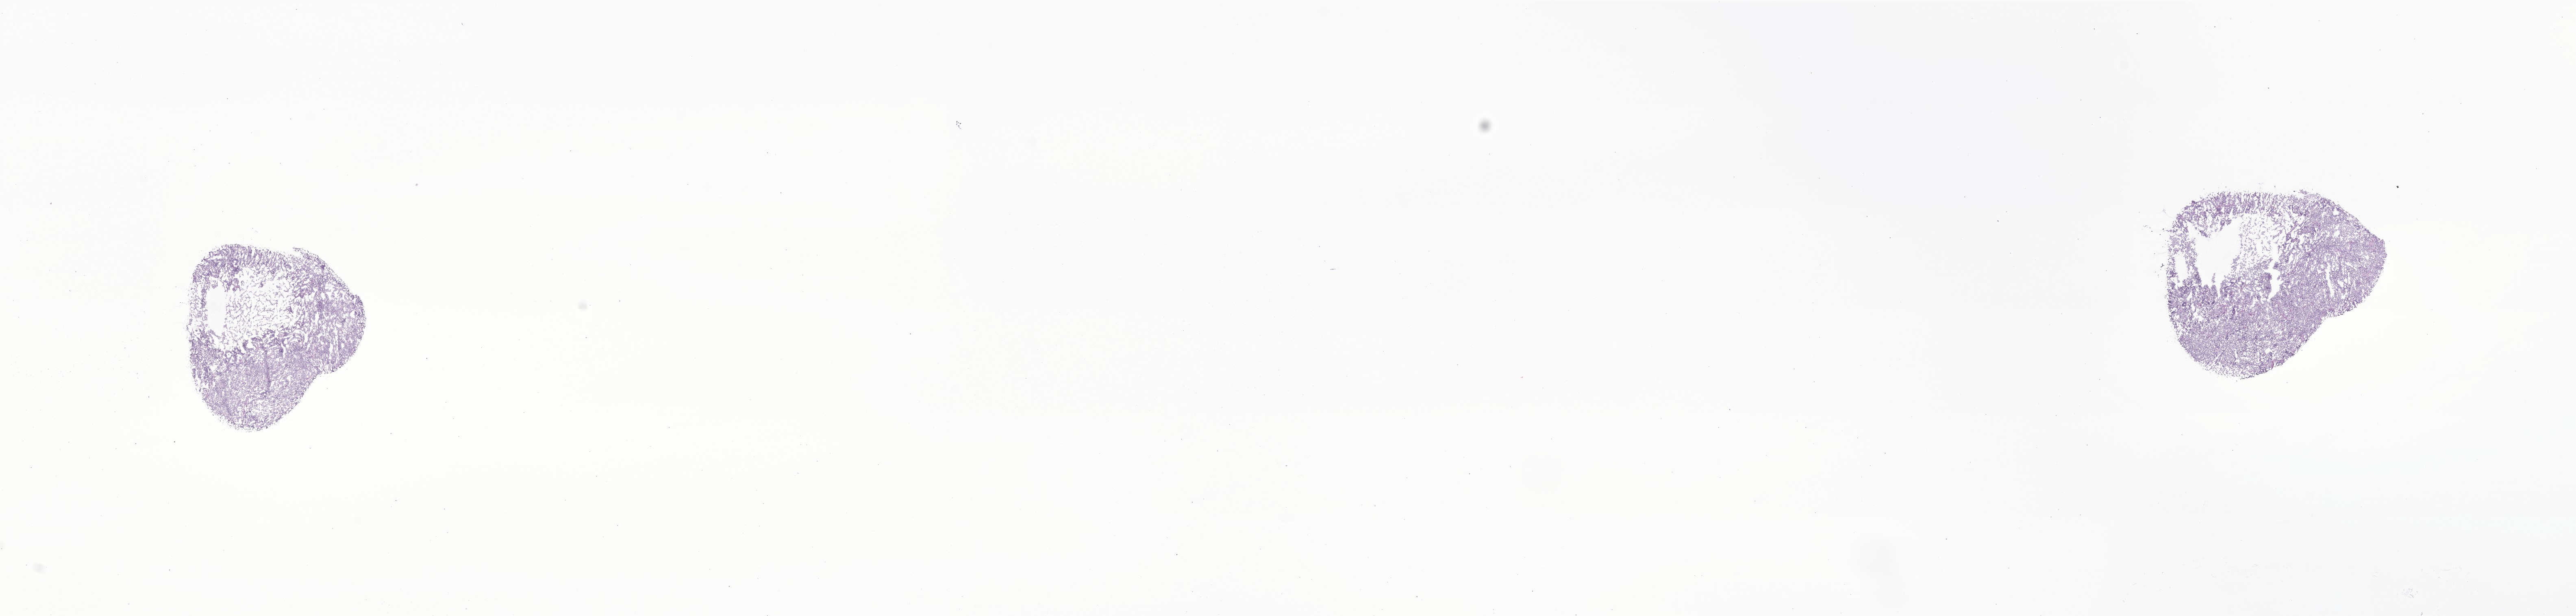
Whole-slide image, H&E stain of tumor tissue from the lower lobe of lung — a low-resolution overview of the entire scanned area, about 26.7 x 6.4 mm, cryosection (OCT / tissue freezing medium). Female patient, age 192 months (16 years).
Diagnosis (ICD-O-3 morphology term): Ewing sarcoma.